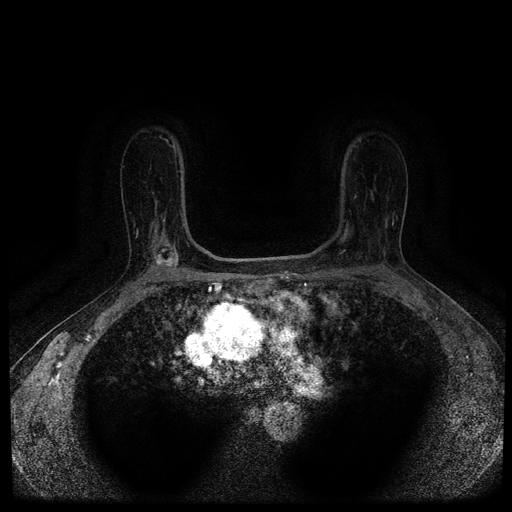
Breast MRI (dynamic contrast-enhanced, multi-phase), one axial slice; position 70 of 116 along the scan axis; dynamic contrast-enhanced series, time point 2 of 5 at this slice position (early post-contrast); 1.5 T; TE 2.7 ms, TR 5.4 ms; 2 mm slice thickness; 512 × 512 image matrix, field of view 330 × 330 mm. Female patient, age 63 years.
Structures marked on this image (semi-automatically segmented with operator editing):
- breast lesion (labelled 'tumour' in the annotation; benign lesions carry a separate 'benign' label): bounding box (x1, y1, x2, y2) in pixels: (154, 242, 180, 270)